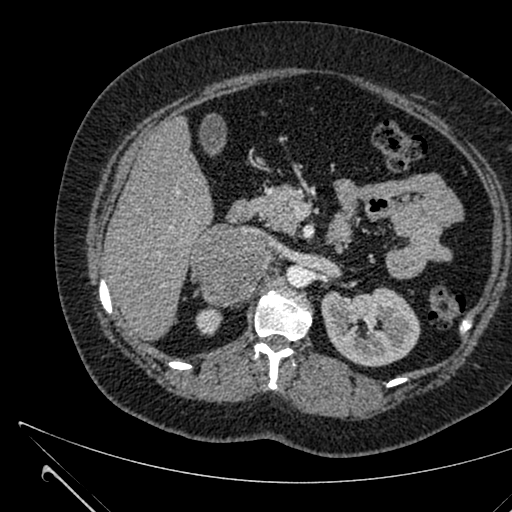
Contrast-enhanced abdominal CT, one axial slice. Position 389 of 731 along the scan axis. 120 kVp. Intravenous contrast given. Soft-tissue window (W 400 / L 40 HU). 1 mm slice thickness. 512 × 512 image matrix, field of view 376 × 376 mm. Female patient, age 36 years. From the clinical record (not read from this slice): diagnosis: adrenocortical carcinoma; tumour side: right adrenal; tumour size at pathology: 10 cm; Ki-67 index: 20 %; stage (as recorded): 4.
Annotated regions visible in this slice (semi-automatic segmentation, software-assisted and operator-edited):
- mass: bounding box [x1, y1, x2, y2] px = [194, 224, 266, 304]